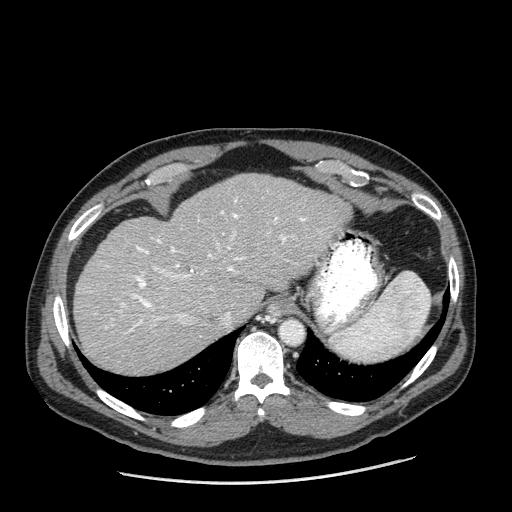
Contrast-enhanced abdominal CT (liver protocol), one axial slice. Position 145 of 198 along the scan axis. Reconstruction kernel STANDARD. 120 kVp. One of 2 acquisitions stored at this slice position. Soft-tissue window (W 400 / L 40 HU). 2.5 mm slice thickness. 512 × 512 image matrix. Case-level facts recorded for this patient, not image findings: diagnosis: hepatocellular carcinoma (patient treated with transarterial chemoembolisation; whether this scan precedes or follows treatment is not stated here); TNM stage (as recorded): Stage-II; Child-Pugh class: A; tumour differentiation: moderately differentiated; tumour nodularity: multinodular.
Structures marked on this image (semi-automatically segmented with operator editing):
- liver parenchyma outside the tumour (the mass and vessels are separate outlines, so this box may not span the whole liver): bounding box <72,173,350,374> (left, top, right, bottom; pixels)
- liver vessels: <90,198,306,332>